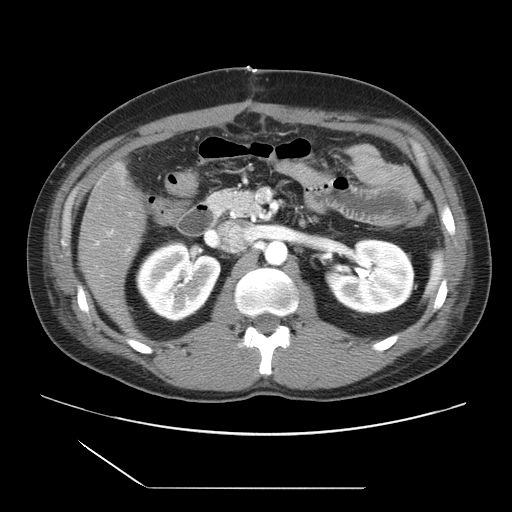
Contrast-enhanced abdominal CT, one axial slice; position 8 of 39 along the scan axis; intravenous contrast given; soft-tissue window (W 400 / L 40 HU); 512 × 512 image matrix. Male patient, age 39 years. From the clinical record (not read from this slice): diagnosis: colorectal cancer liver metastases, imaged before liver resection.
Structures marked on this image (expert manual segmentation):
- liver: box from (x=80, y=166) to (x=146, y=332) px
- portal vein (with intrahepatic branches): (x=95, y=230)–(x=130, y=276)